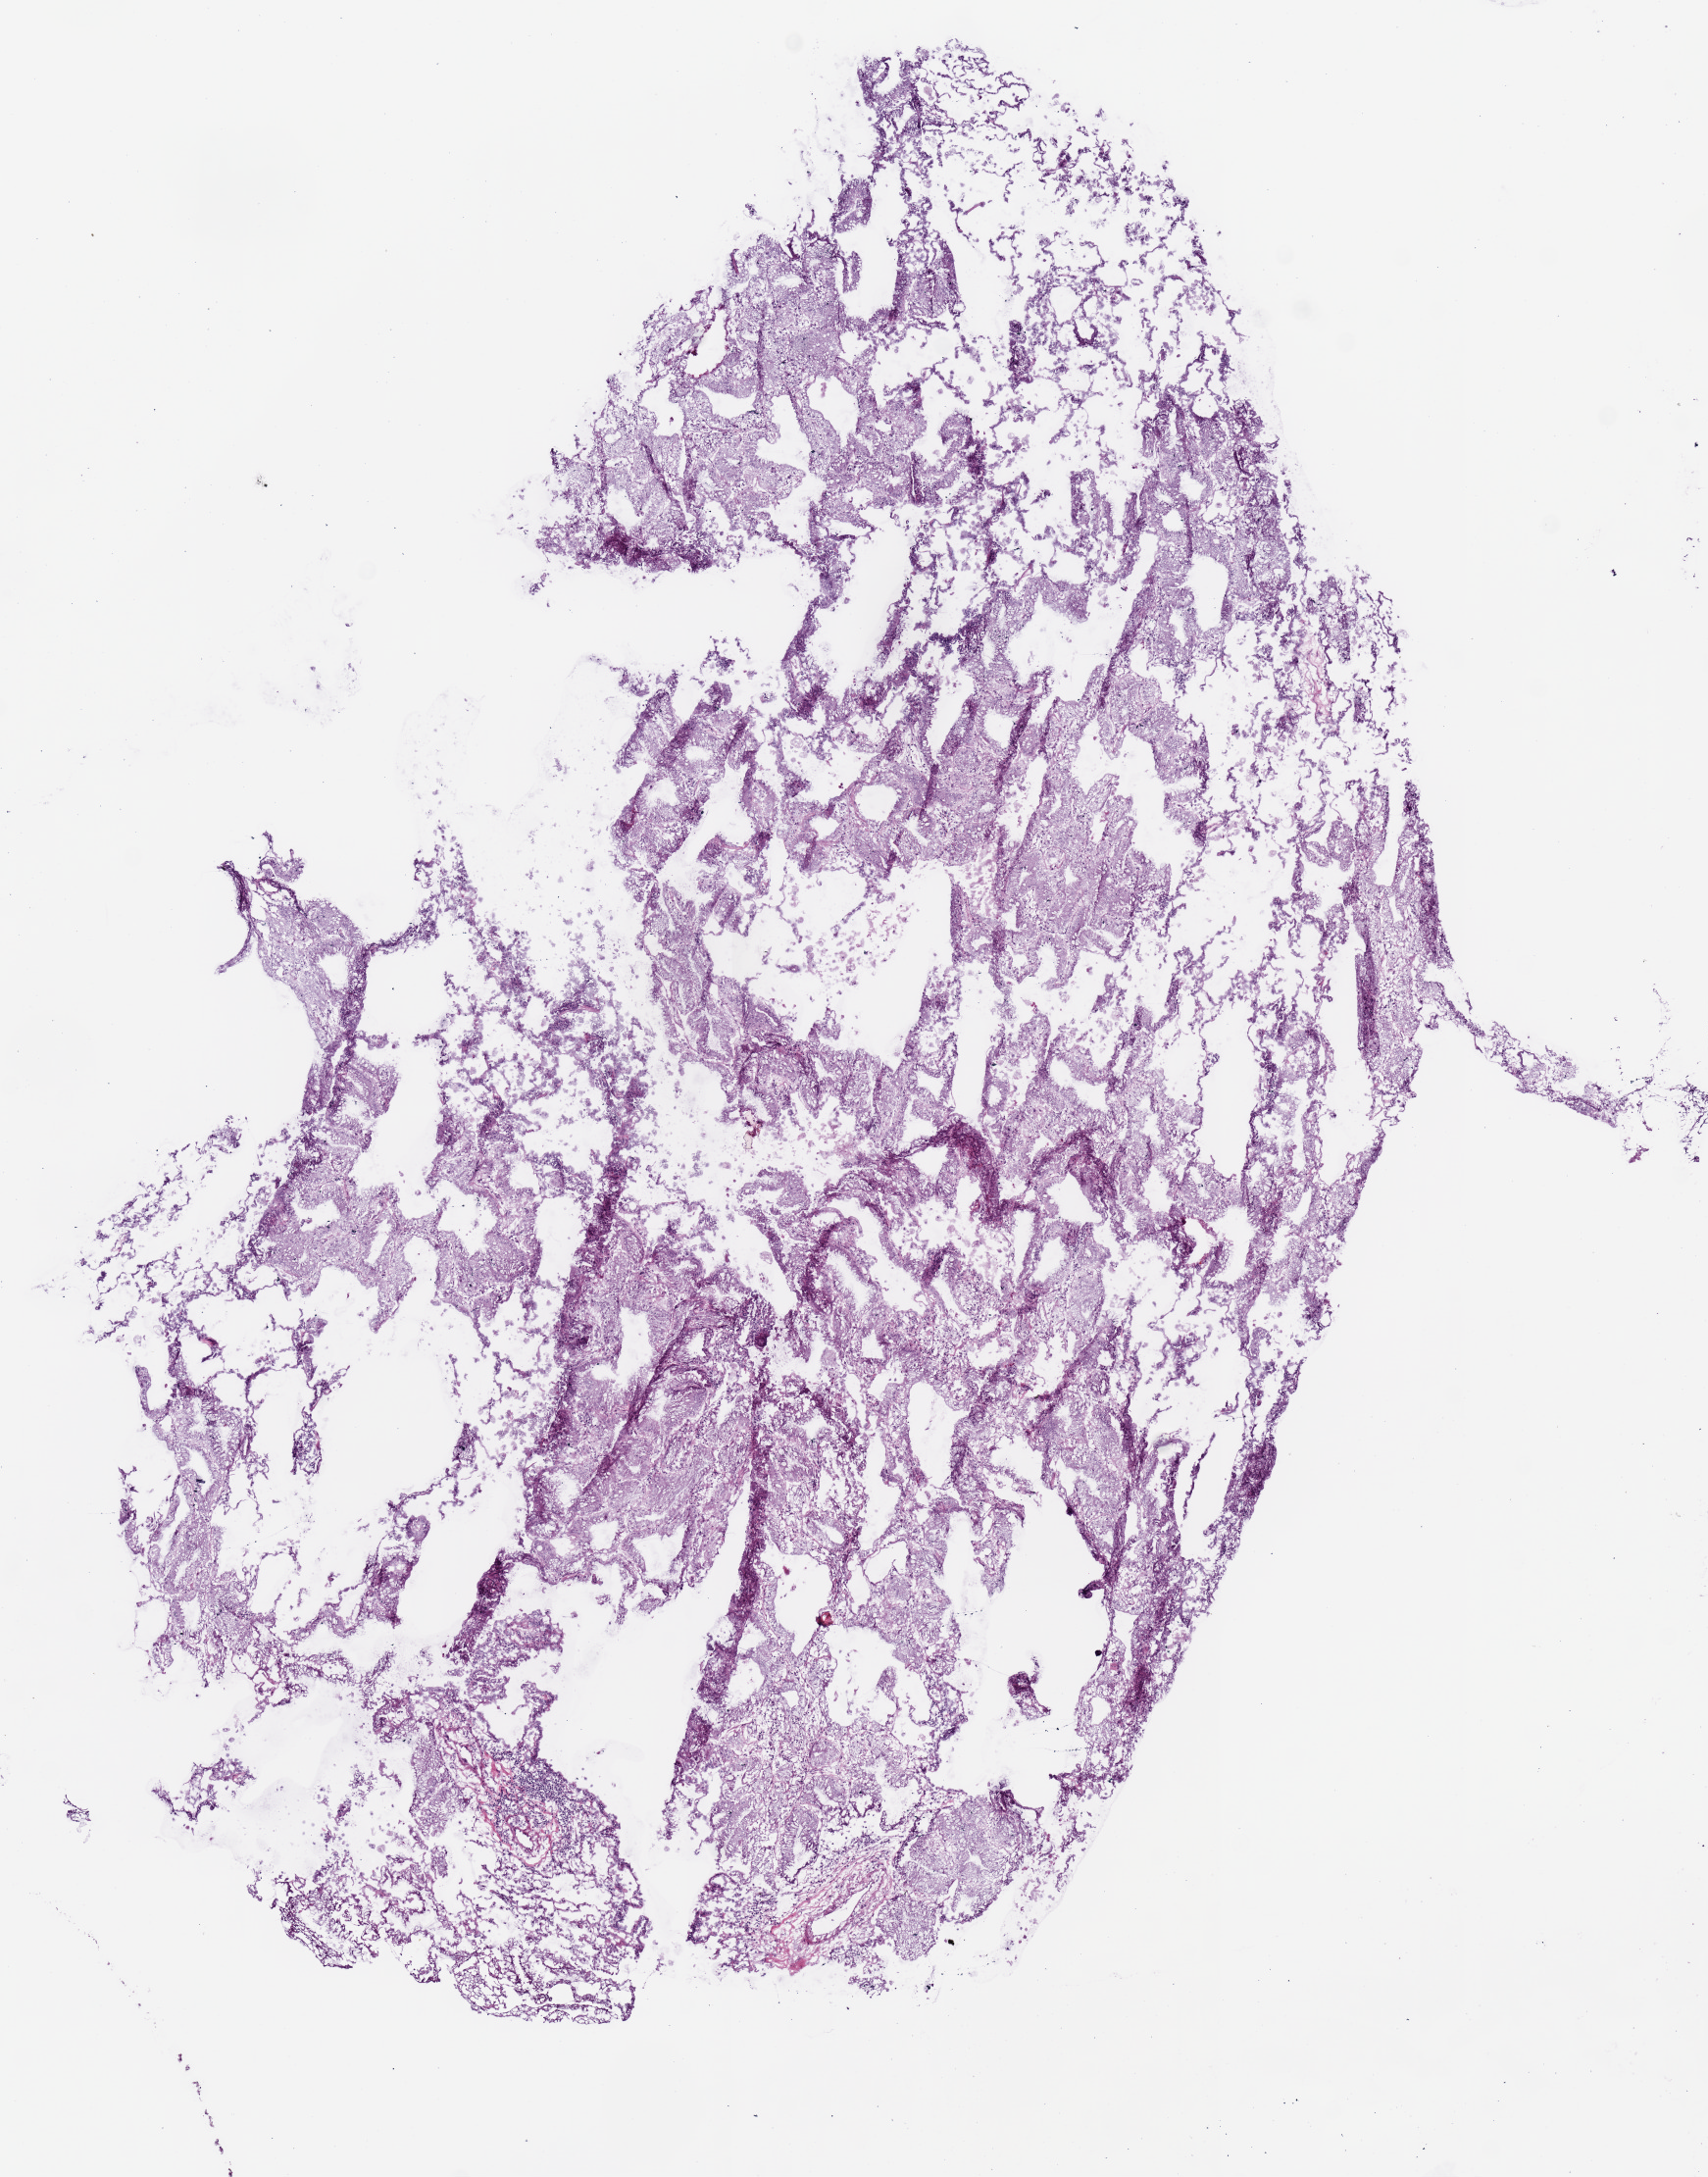
H&E whole-slide image, a low-resolution overview of the entire scanned area, about 6.9 x 8.8 mm, frozen section, sample: primary tumour, lung. Female, age 77 years at initial diagnosis. Slide review estimates, as recorded: tumour cells 90%, tumour nuclei 80%, normal cells 0%, stromal cells 10%, necrosis 0%.
AJCC pathologic stage: IIB. Histologic diagnosis: Mucinous adenocarcinoma (lower lobe, lung).